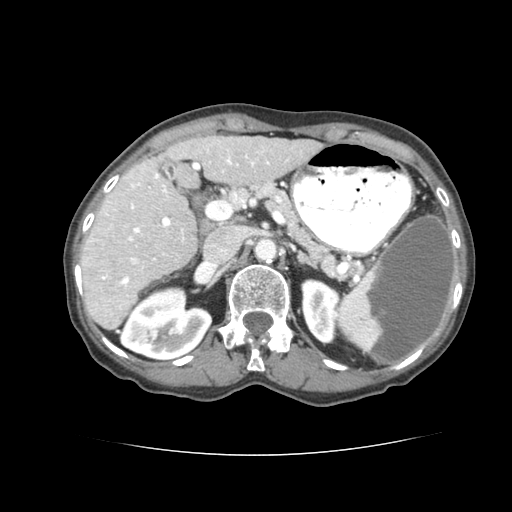
Contrast-enhanced abdominal CT (liver protocol), one axial slice; slice 41 of 77 in the series (ordered by position); 120 kVp; soft-tissue window (W 400 / L 40 HU); 512 × 512 image matrix. From the clinical record (not read from this slice): diagnosis: hepatocellular carcinoma (patient treated with transarterial chemoembolisation; whether this scan precedes or follows treatment is not stated here); TNM stage (as recorded): Stage-I.
Annotated regions visible in this slice (semi-automatic segmentation, software-assisted and operator-edited):
- liver parenchyma outside the tumour (the mass and vessels are separate outlines, so this box may not span the whole liver): bounding box (x1, y1, x2, y2) in pixels: (78, 138, 318, 328)
- liver vessels: (98, 163, 270, 275)